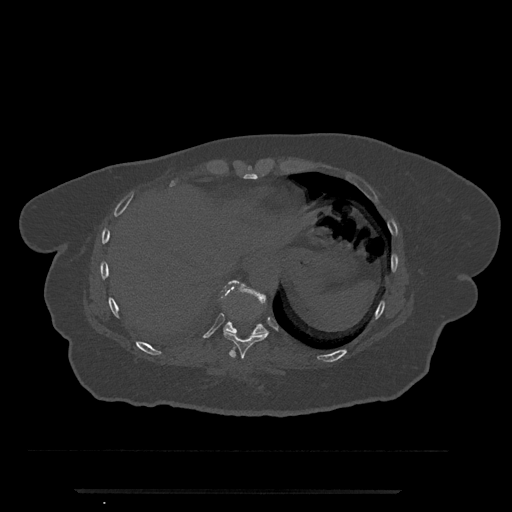
CT including the spine, one axial slice; slice 320 of 797 in the series (ordered by position); reconstruction kernel Br40s/3; 120 kVp; bone window (W 1800 / L 400 HU); 512 × 512 image matrix. Female patient, age 51 years. Case-level facts recorded for this patient, not image findings: primary cancer: neuro; vertebrae with lytic lesions (as recorded): T8.
Structures marked on this image (semi-automatic segmentation, software-assisted and operator-edited):
- T10 vertebra: bounding box (x1, y1, x2, y2) in pixels: (223, 280, 267, 336)
- T9 vertebra: (223, 331, 269, 359)